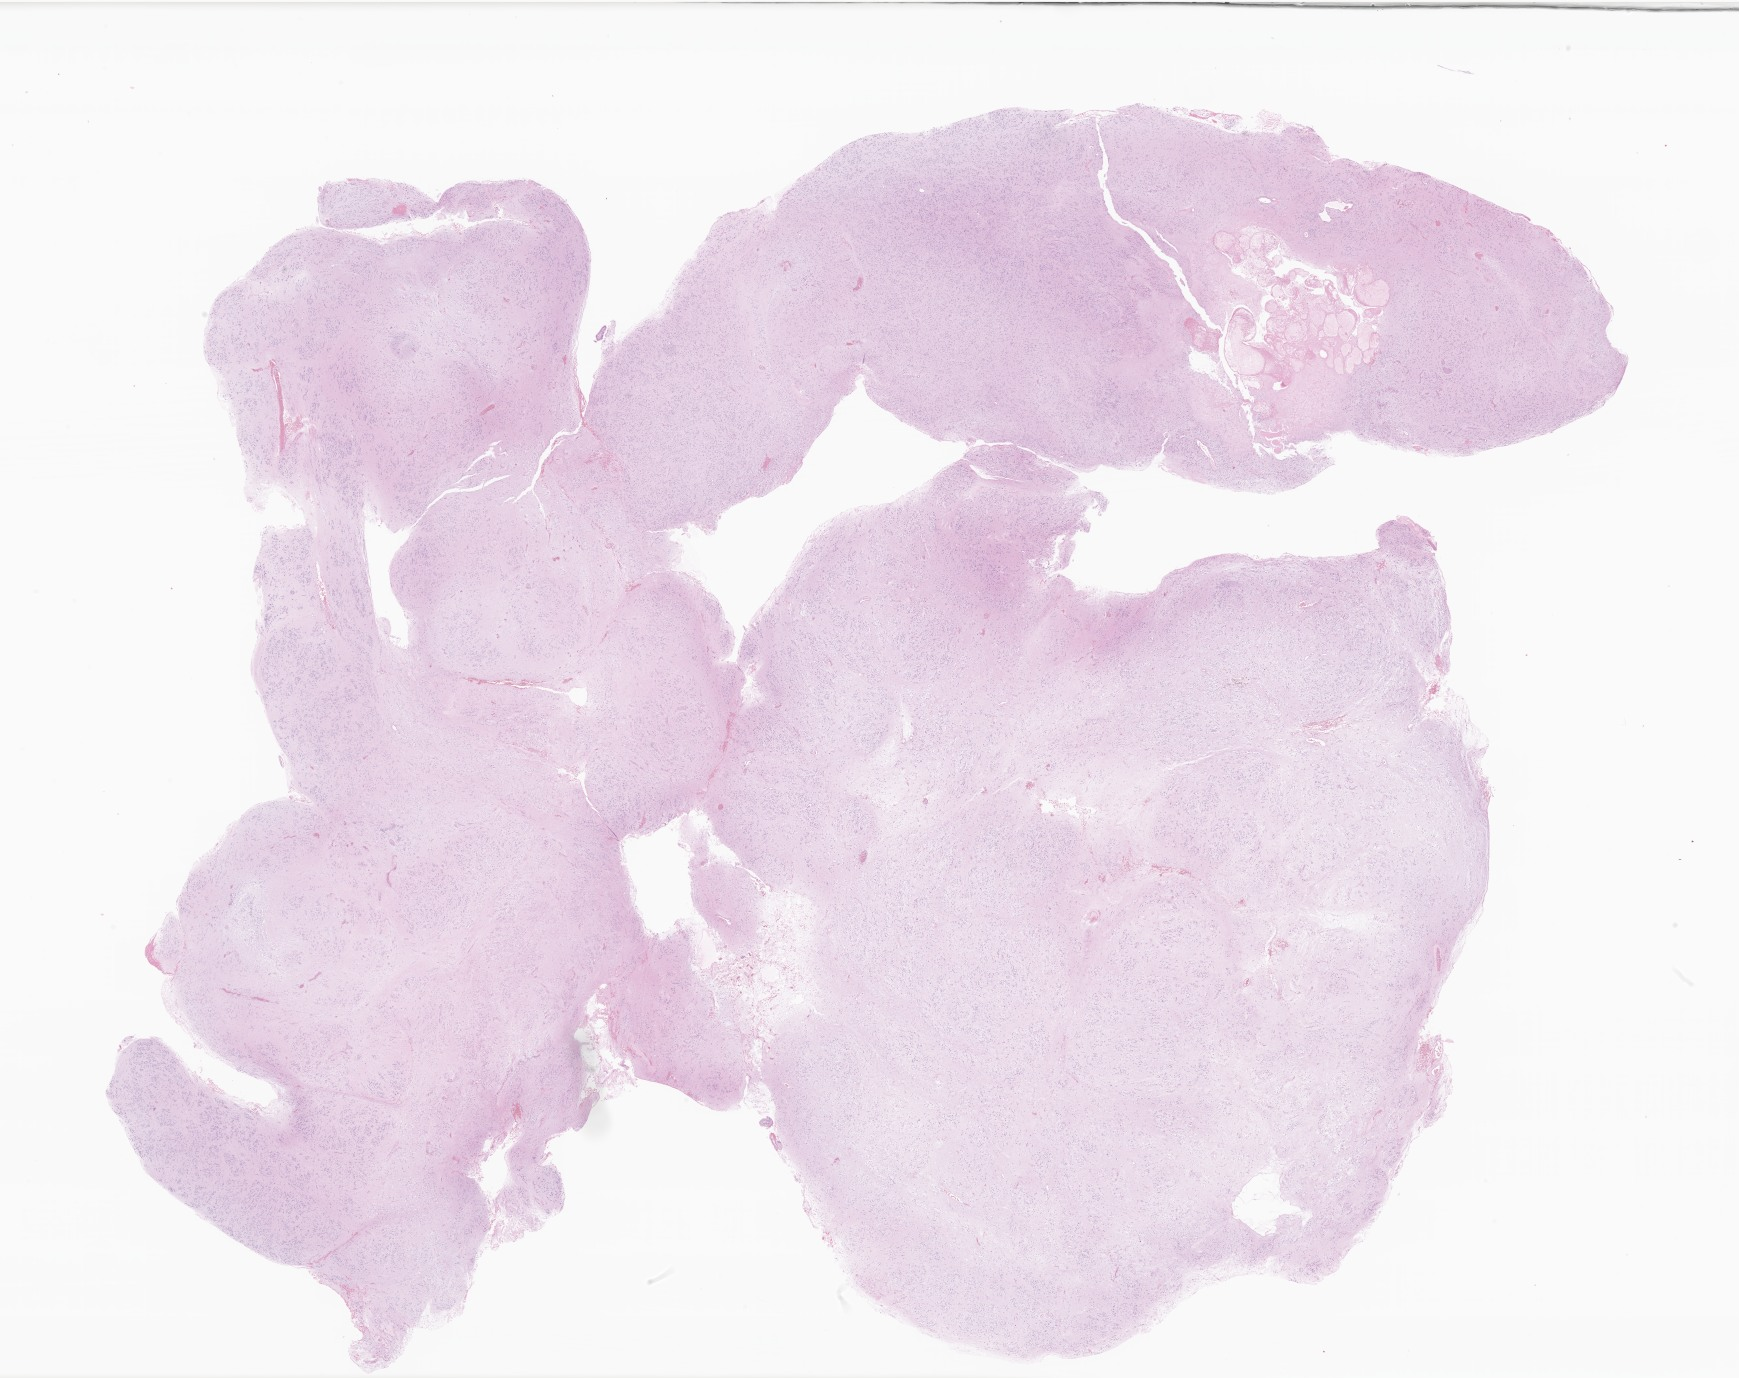
H&E whole-slide image of tumor tissue from the brain — low-resolution overview of the scanned area, about 29.3 x 23.2 mm, formalin-fixed, paraffin-embedded (FFPE) tissue. Female patient, age 205 months (17 years 1 month).
- recorded diagnosis: Subependymoma